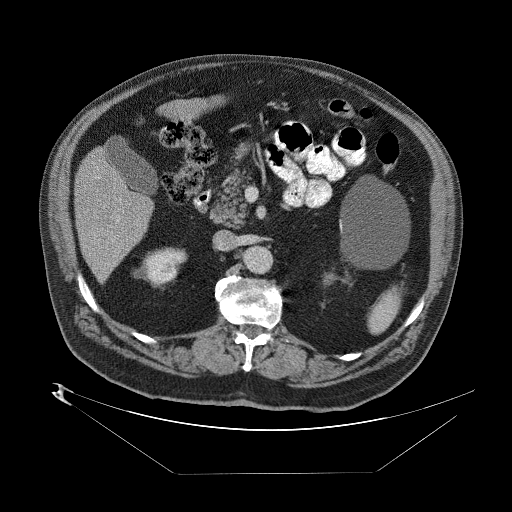
Contrast-enhanced abdominal CT (liver protocol), one axial slice. Position 29 of 89 along the scan axis. Reconstruction kernel STANDARD. One of 2 acquisitions stored at this slice position. Soft-tissue window (W 400 / L 40 HU). 2.5 mm slice thickness. 512 × 512 image matrix, field of view 480 × 480 mm. Case-level facts recorded for this patient, not image findings: diagnosis: hepatocellular carcinoma (patient treated with transarterial chemoembolisation; whether this scan precedes or follows treatment is not stated here); TNM stage (as recorded): Stage-II; Child-Pugh class: B; tumour differentiation: moderately differentiated; tumour nodularity: multinodular.
Annotated regions visible in this slice (semi-automatically segmented with operator editing):
- abdominal aorta: bounding box <246,249,270,274> (left, top, right, bottom; pixels)
- liver parenchyma outside the tumour (the mass and vessels are separate outlines, so this box may not span the whole liver): <72,142,152,284>
- liver vessels: <84,215,121,244>